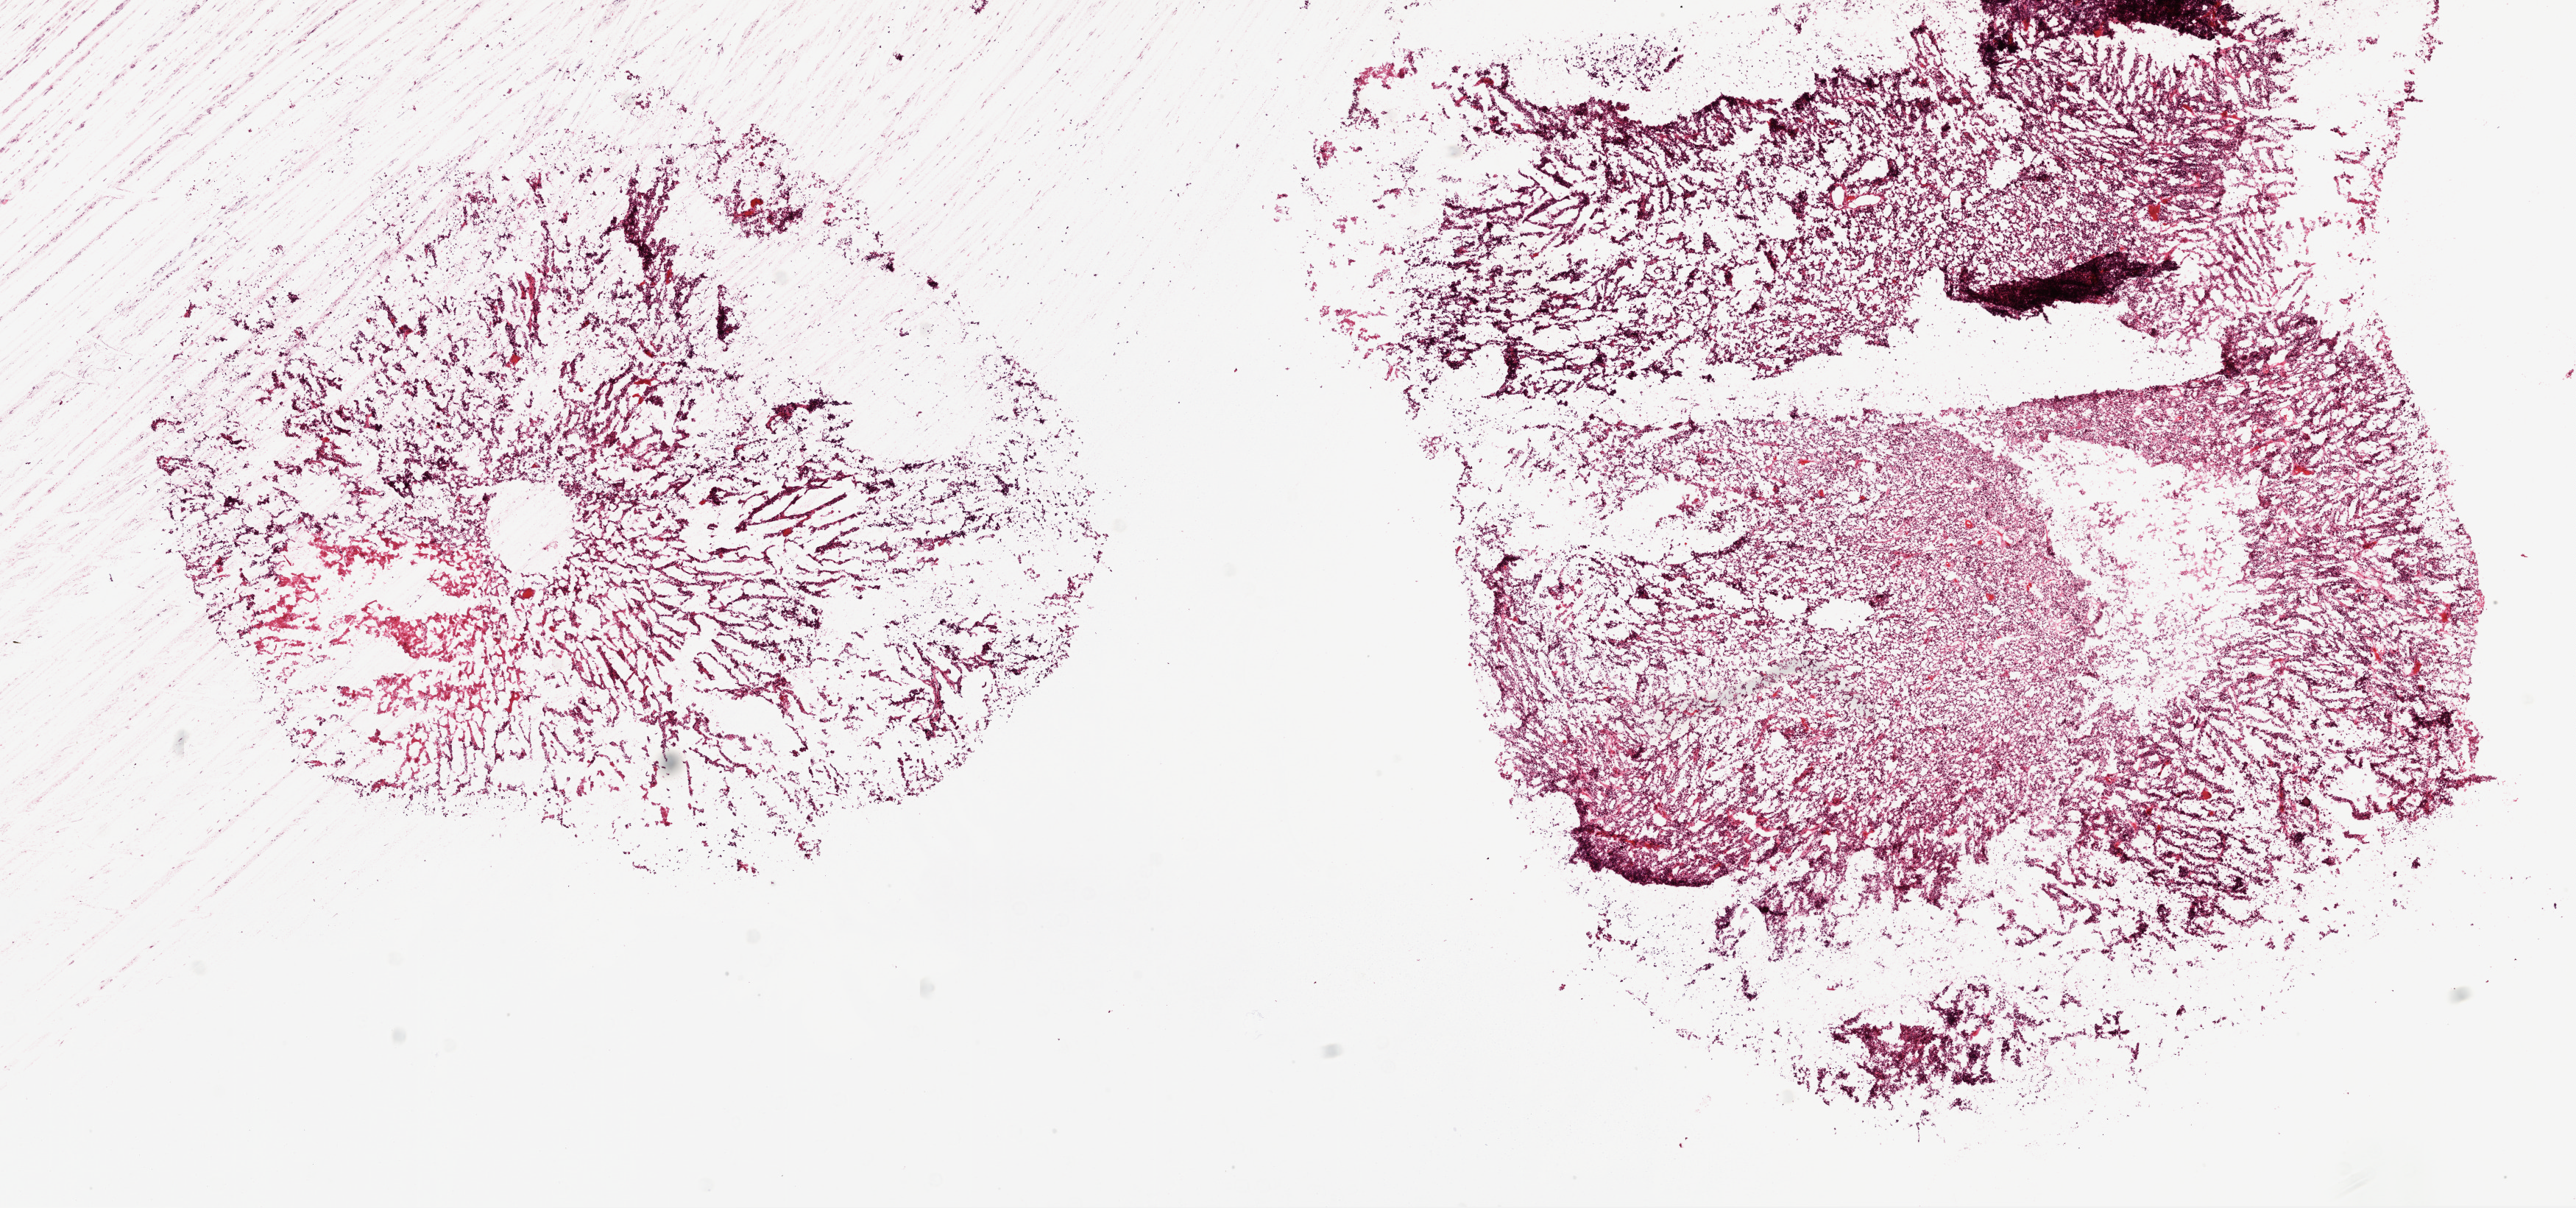
Digitized H&E-stained tissue section (whole slide) — low-resolution overview of the scanned area, about 14.0 x 6.6 mm (slide scanned at 20x); frozen section from the top of the tissue portion; brain, primary tumour sample. Female patient; age at initial diagnosis 44 years. Composition of this section per pathologist review: tumour cells 70%, tumour nuclei 85%.
Histologic diagnosis: Glioblastoma.